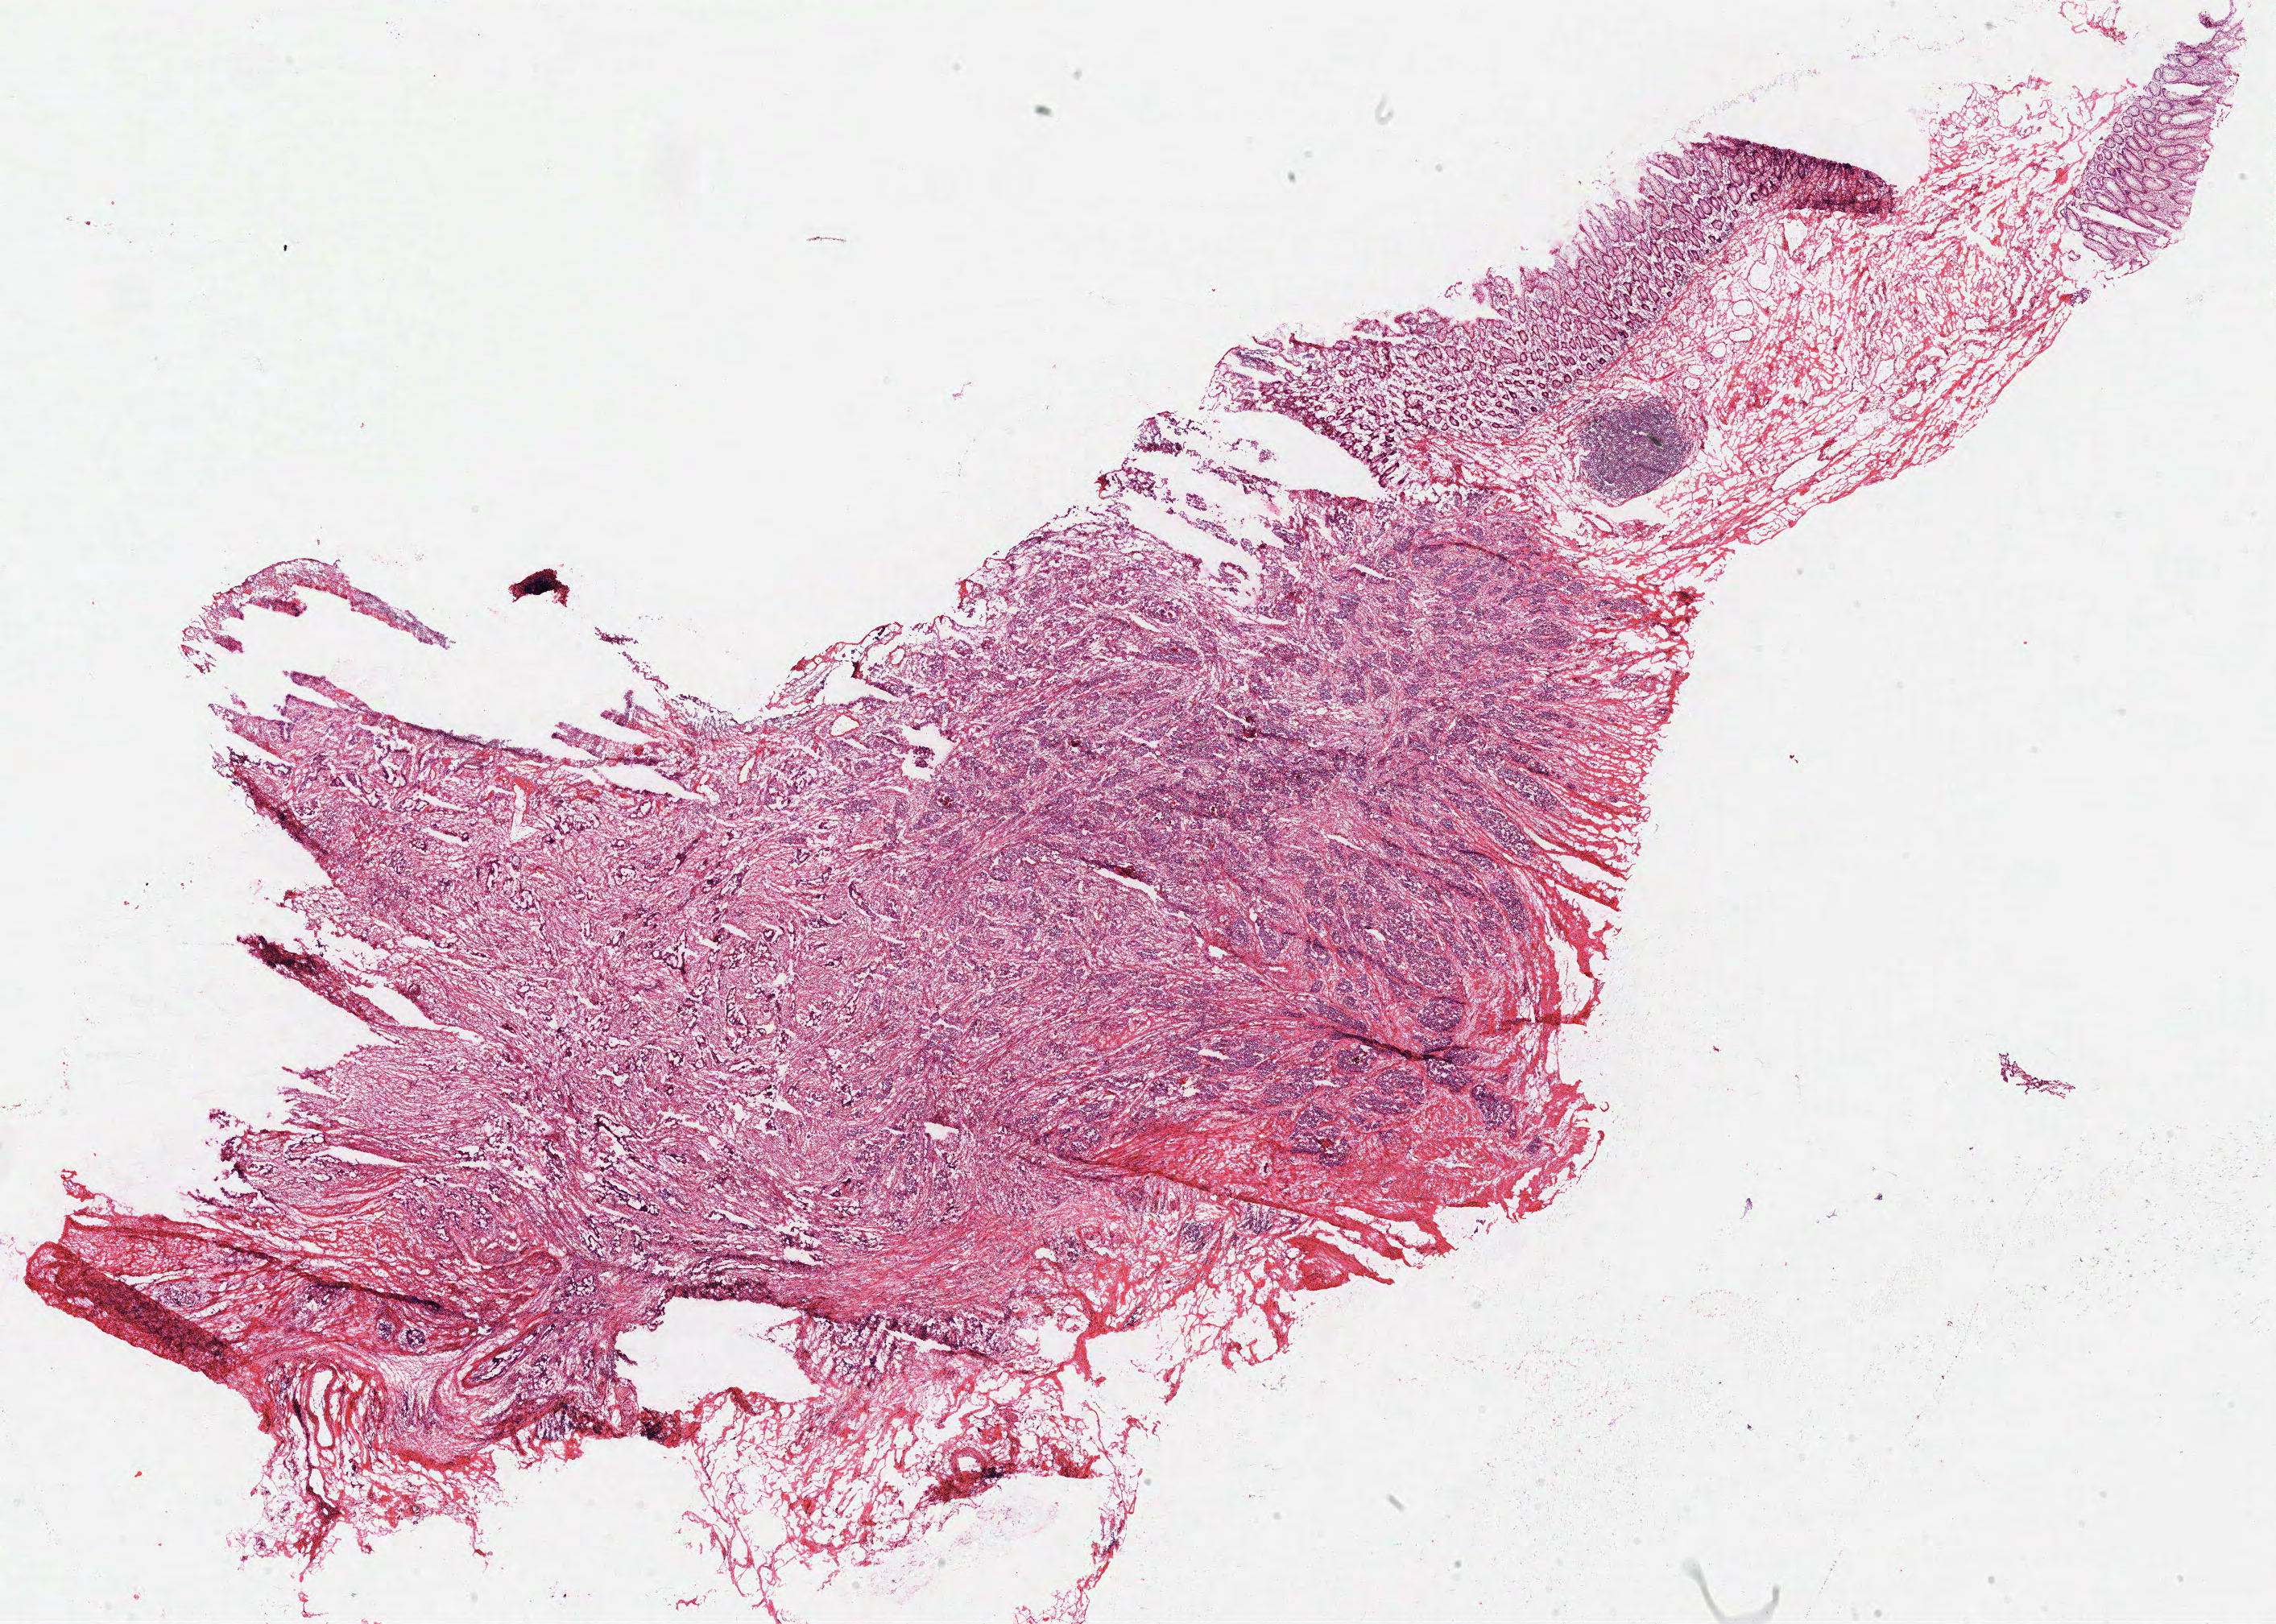
Whole-slide histology image, H&E-stained, a low-resolution overview of the entire scanned area, about 22.3 x 15.9 mm. Frozen section from the top of the tissue portion. Rectum, primary tumour sample. Male patient; age at initial diagnosis 71 years. Composition of this section per pathologist review: tumour cells 74%, tumour nuclei 80%, normal cells 5%, stromal cells 20%, necrosis 1%.
- AJCC pathologic stage: IVA (7th edition)
- TNM: T3 N1 M1
- pathologic diagnosis: Adenocarcinoma, NOS (rectosigmoid junction)
- lymph nodes positive (case pathology): 1 of 12 examined